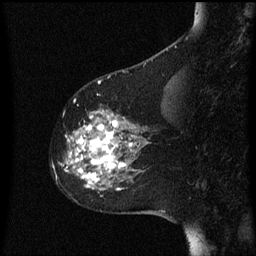
Breast MRI (dynamic contrast-enhanced), one sagittal slice. Position 19 of 60 along the scan axis. Dynamic contrast-enhanced series, image 2 of 3 at this slice position (ordered by acquisition). 1.5 T. TE 4.2 ms, TR 8 ms. 2 mm slice thickness. 256 × 256 image matrix, field of view 200 × 200 mm. Female patient, age 60 years.
Annotated regions visible in this slice (semi-automatically segmented with operator editing):
- analysis volume of interest (the breast-tissue region the enhancement analysis was run in; not a lesion): bounding box [x1, y1, x2, y2] px = [54, 108, 151, 197]
- tumour enhancement mask (voxels above the 70 % enhancement threshold inside the analysis volume of interest): [66, 112, 137, 191]